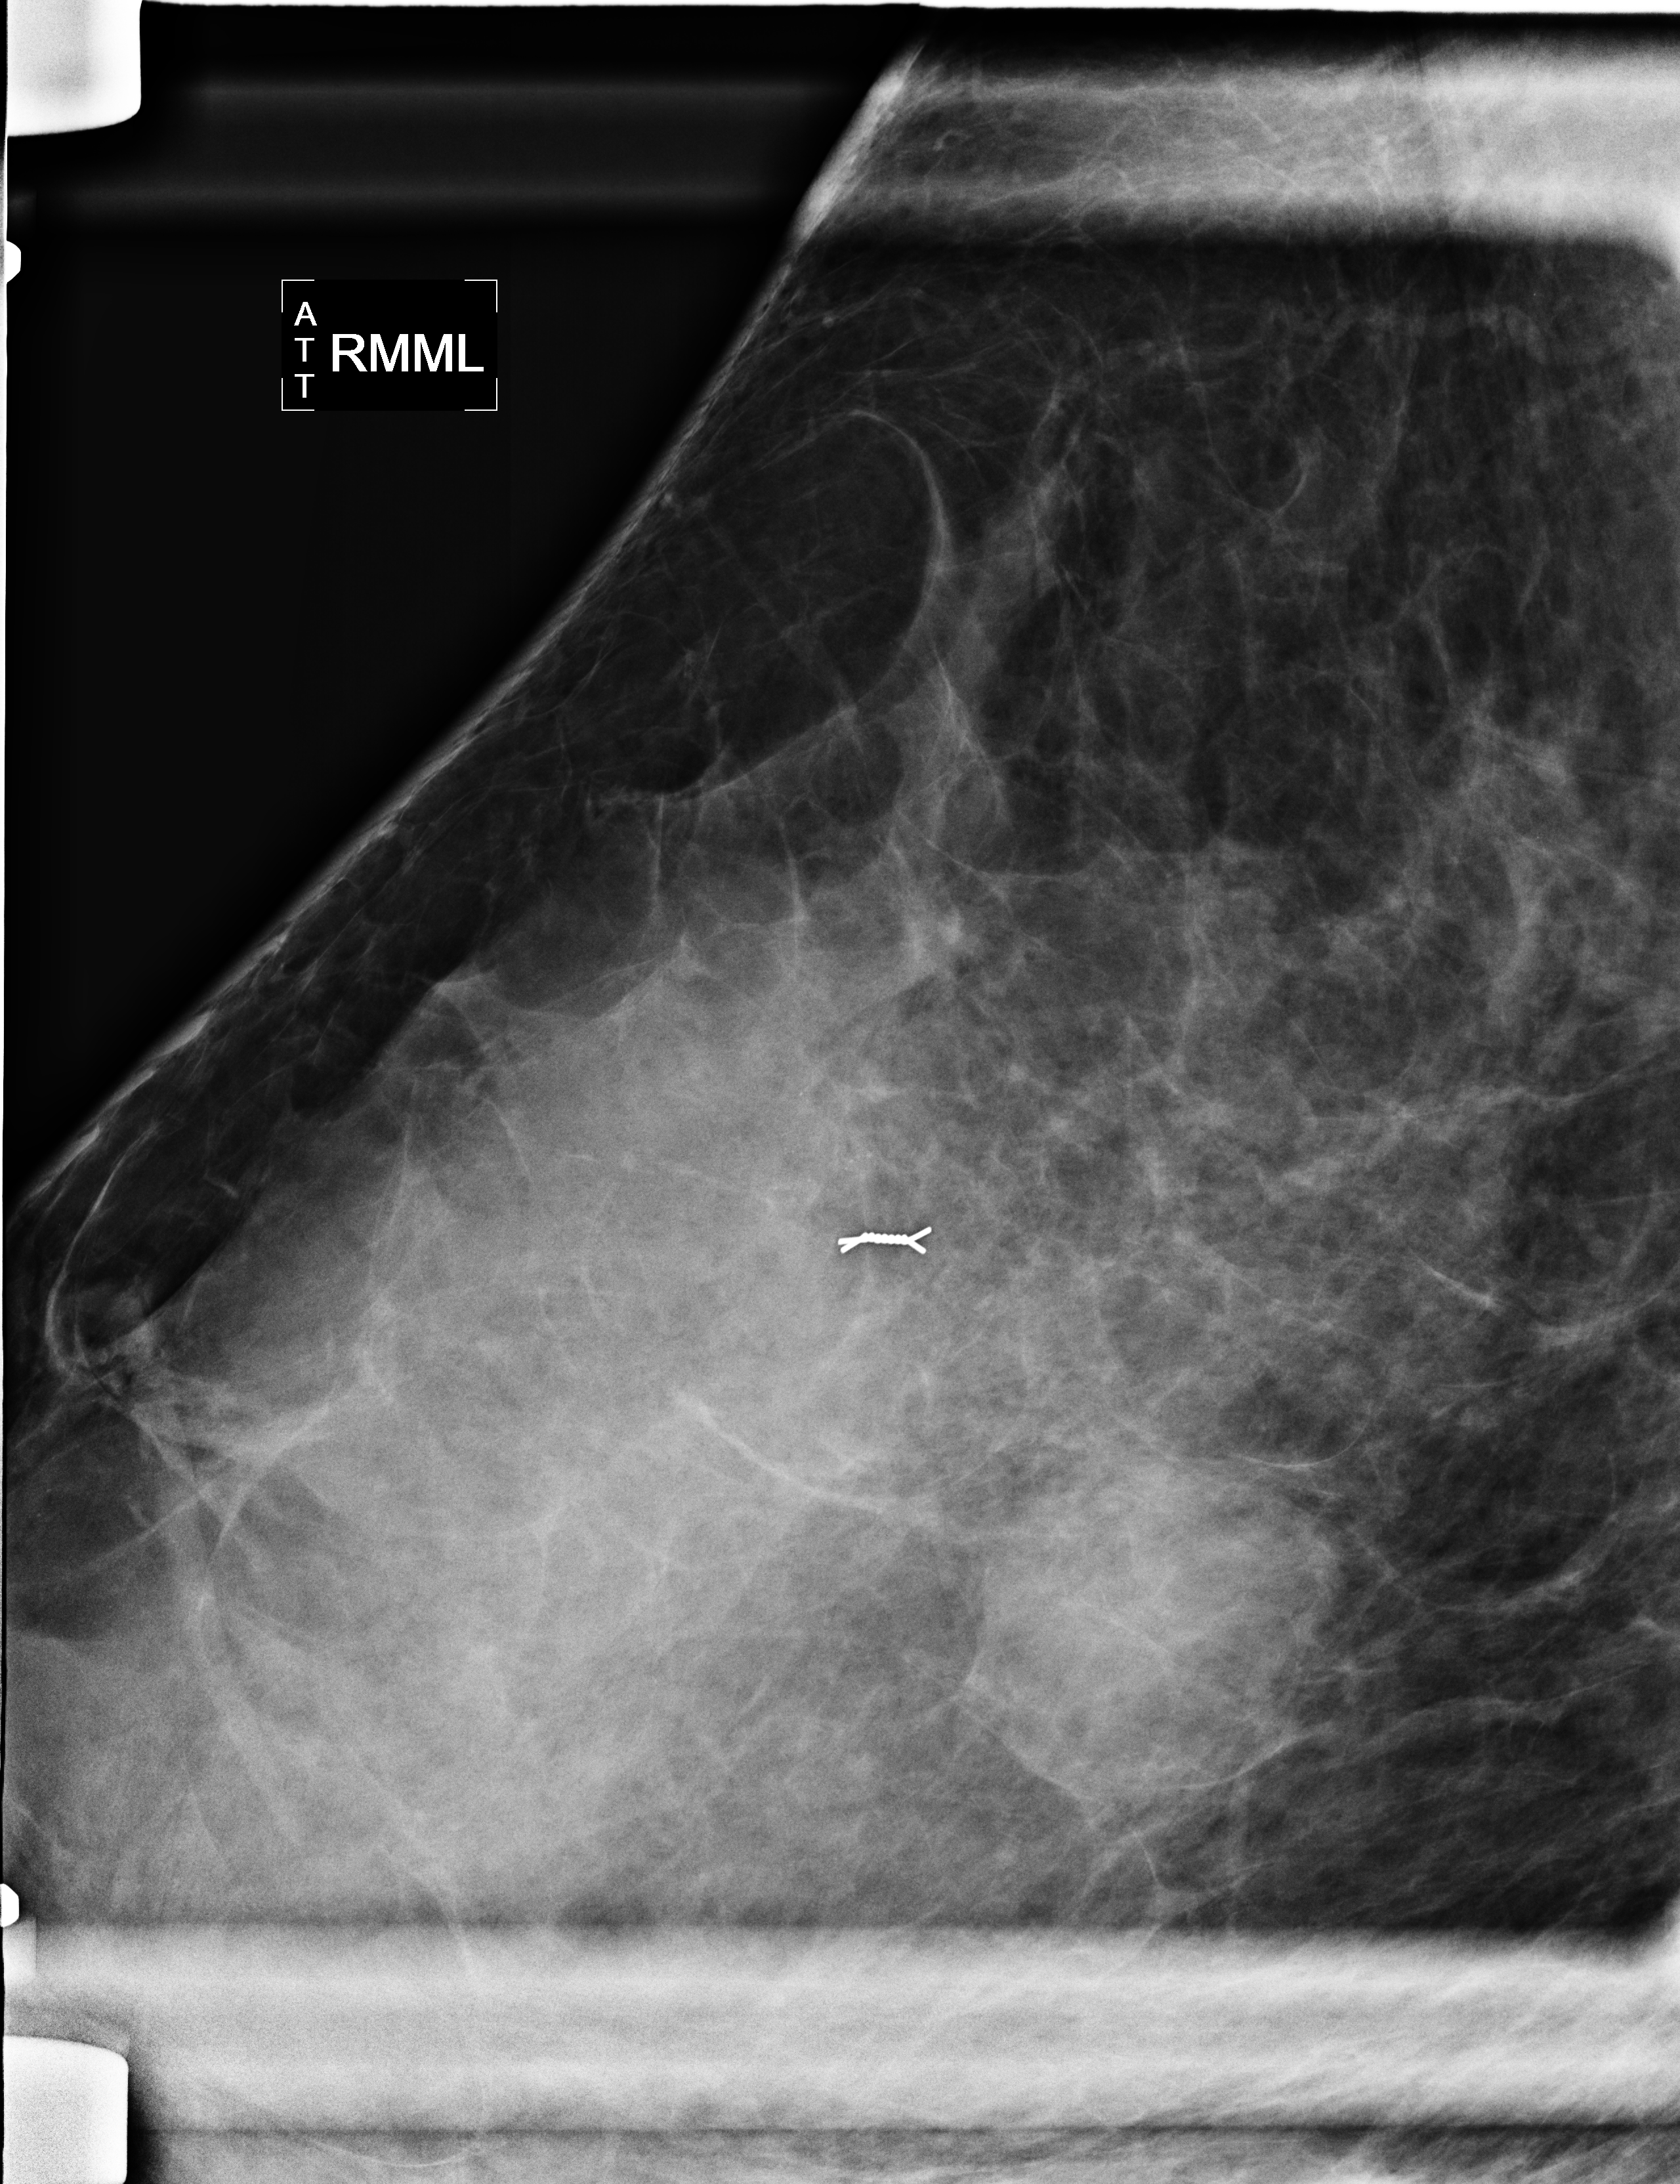
Mammogram, right breast, ML view.
Patient-level pathology facts (clinical record, not image findings): pathology diagnosis: benign fibroadenoma (right breast); pathology report notes: RIGHT BREAST CALCIFICATION WITH NEEDLE LOCATION: FIBROADENOMA (1.9CM). REMAINING BREAST TISSUE WITH ADENOSIS, FOCAL FIBROADENOMATOUS CHANGES, APOCRINE METAPLASIA, FIBROCYSTIC CHANGES, SMALL INTRADUCTAL PAPILLOMAS, AND USUAL TYPE DUCTAL HYPERPLASIA. MICROCALCIFICATIONS ASSOCIATED WITH BENIGN BREAST TISSUE ARE IDENTIFIED. NO IN-SITU OR INVASIVE CARCINOMA.